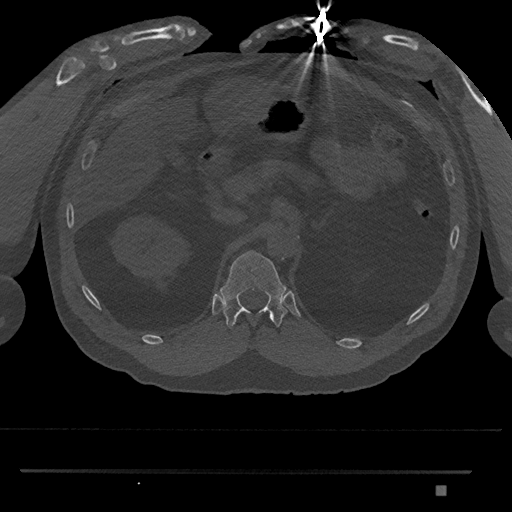
CT including the spine, one axial slice; position 898 of 1134 along the scan axis; bone window (W 1800 / L 400 HU); 512 × 512 image matrix, field of view 429 × 429 mm. Patient: male, 65 years. Case-level facts recorded for this patient, not image findings: primary cancer: prostate.
Outlined on this slice (semi-automatic segmentation, software-assisted and operator-edited):
- T12 vertebra: bounding box (x1, y1, x2, y2) in pixels: (220, 250, 288, 328)